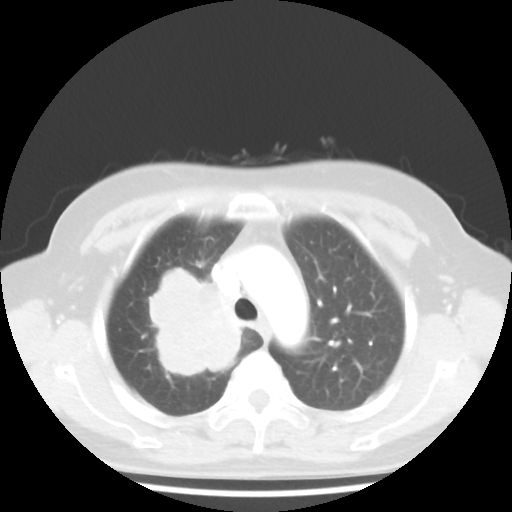
Chest CT, one axial slice; position 33 of 44 along the scan axis; 100 kVp; lung window (W 1500 / L -600 HU); 512 × 512 image matrix. Patient: female, 62 years. From the clinical record (not read from this slice): clinical TNM (as recorded): T3 N0 M0; histopathological grade: G3.
Outlined on this slice (bounding box drawn by a radiologist):
- lung tumour (recorded histology: small cell carcinoma): box from (x=137, y=270) to (x=248, y=384) px